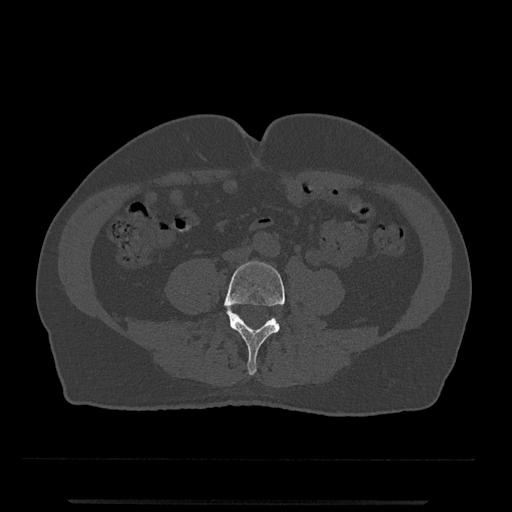
CT including the spine, one axial slice. Position 131 of 797 along the scan axis. Reconstruction kernel Br40s/3. Bone window (W 1800 / L 400 HU). 0.5 mm slice thickness. 512 × 512 image matrix, field of view 419 × 419 mm. Male patient, age 63 years. Case-level facts recorded for this patient, not image findings: primary cancer: prostate.
Outlined on this slice (semi-automatically segmented with operator editing):
- L4 vertebra: bounding box [x1, y1, x2, y2] px = [220, 261, 285, 375]